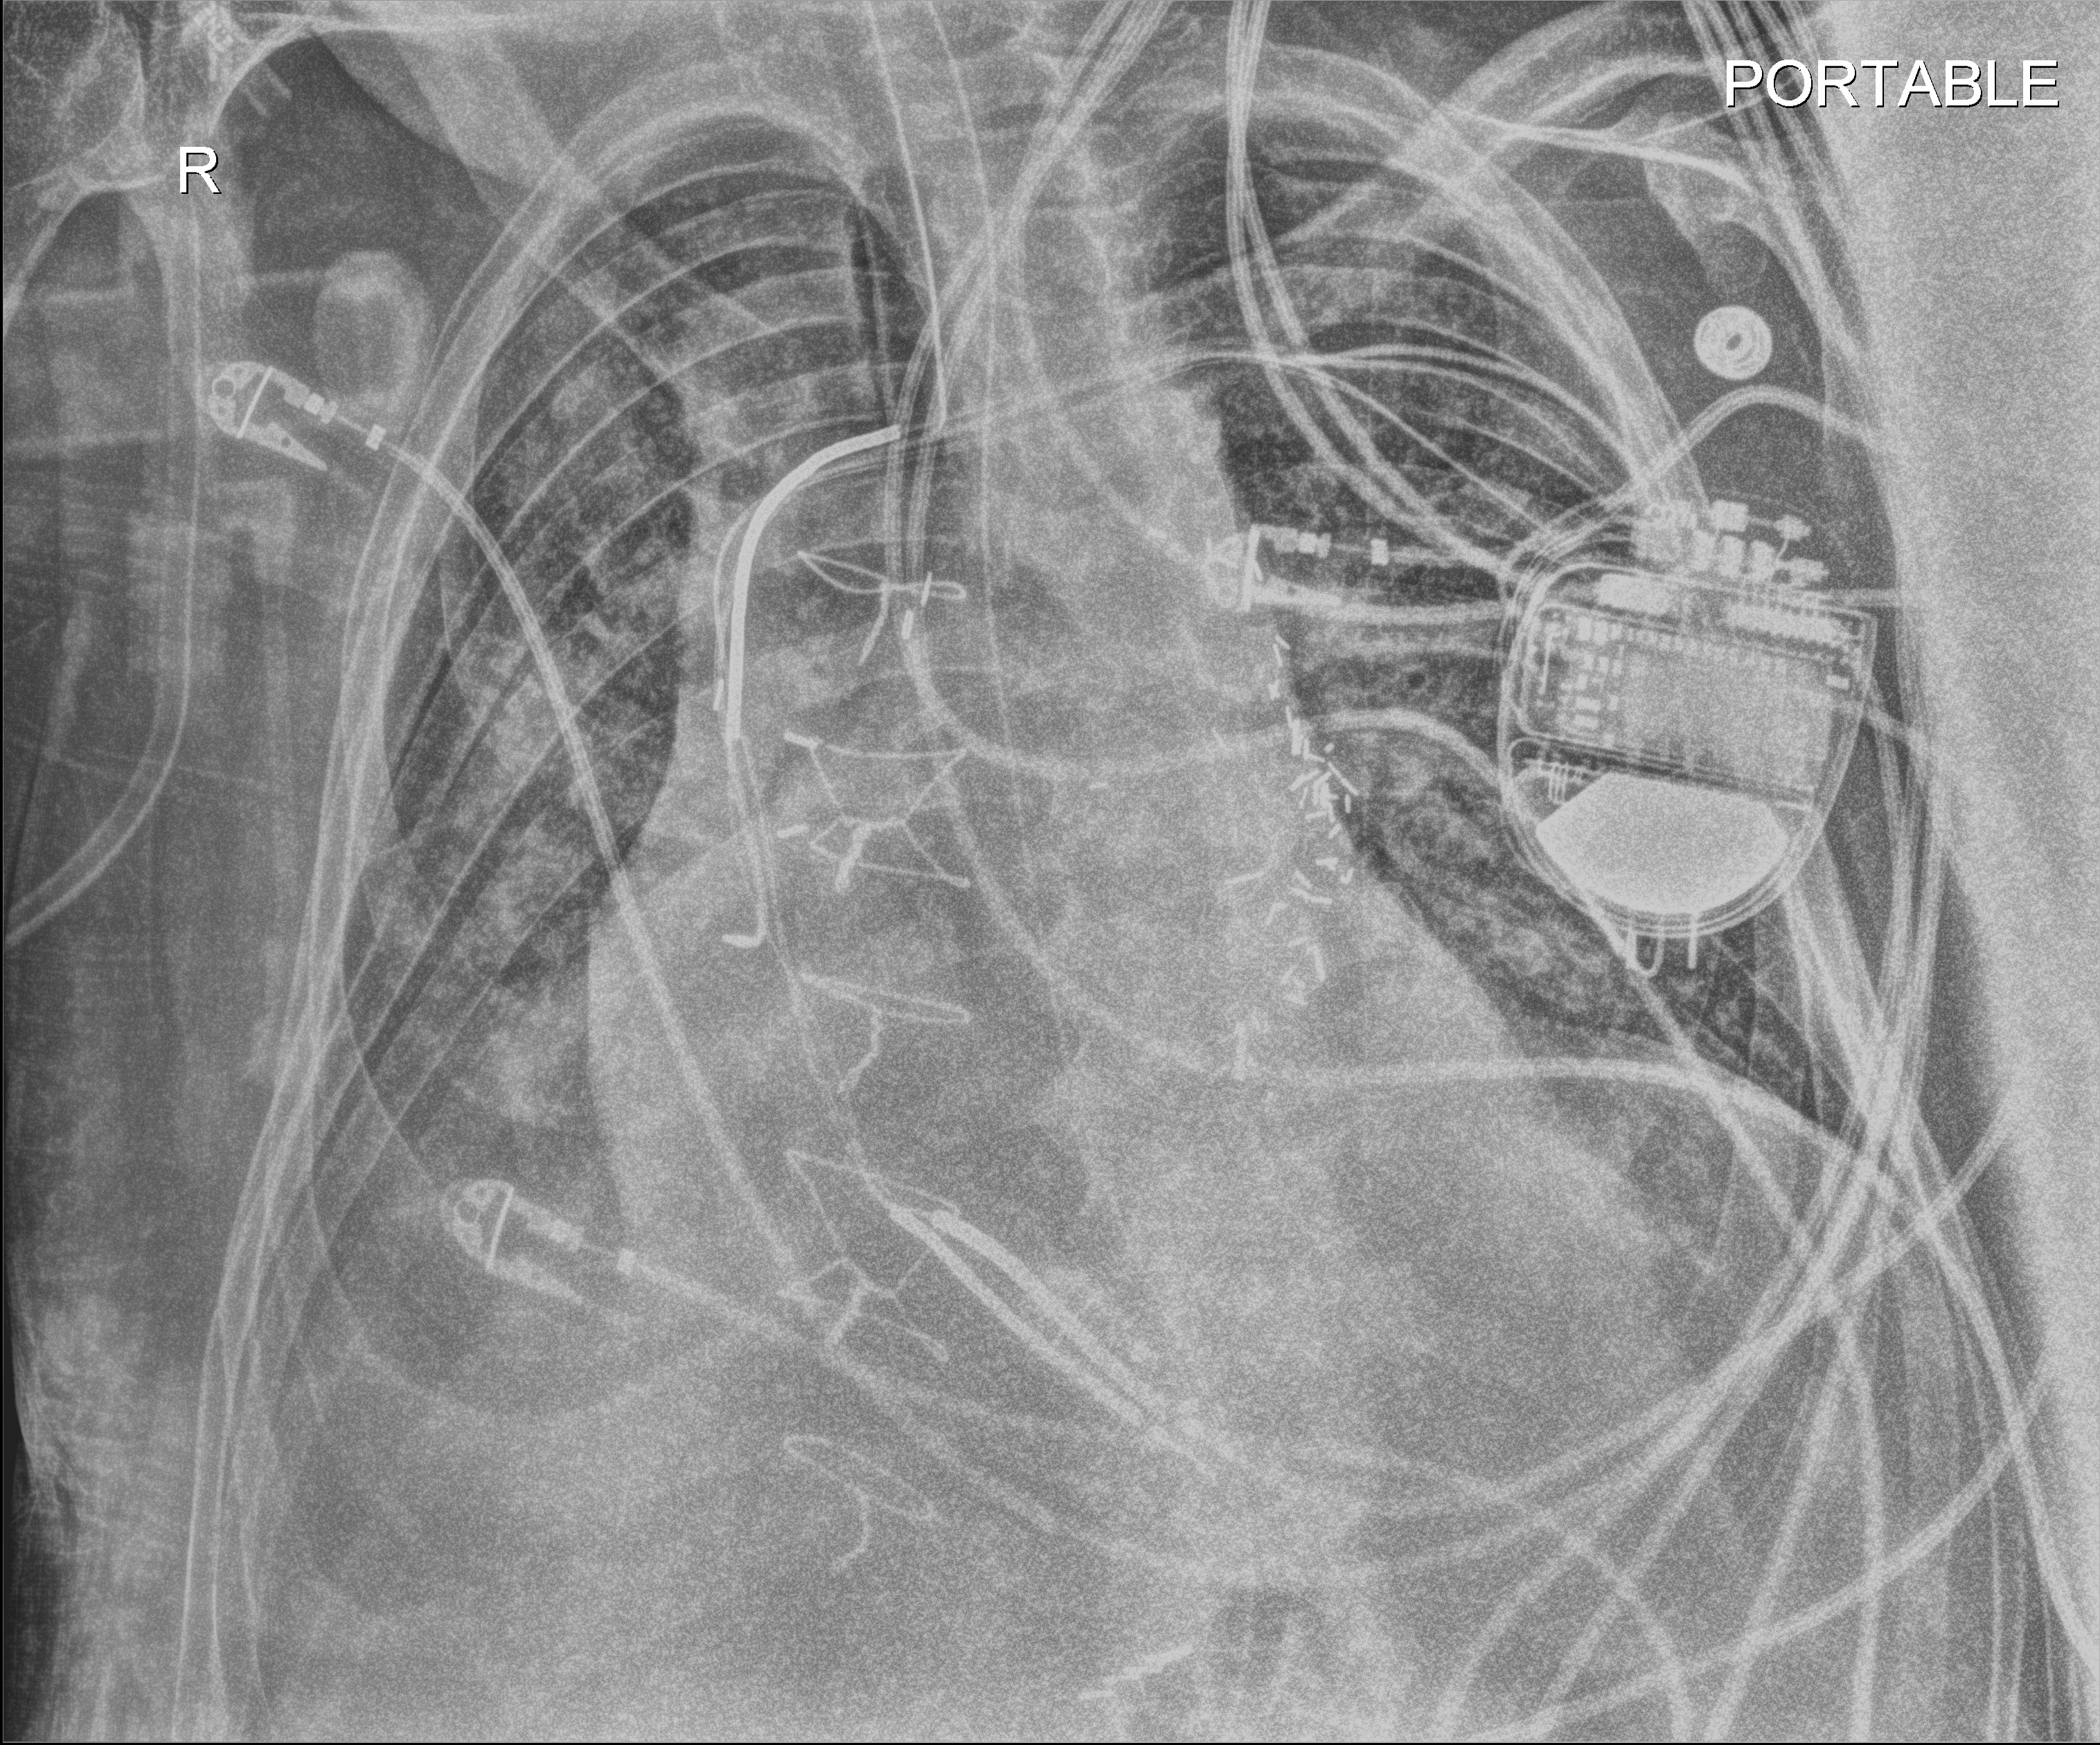
Portable chest radiograph; anteroposterior (AP) projection. Male patient hospitalised with COVID-19, age 60–74 years.
Hospital-stay facts (about this admission, not read from this image; timing relative to this image not recorded): admitted to intensive care during this hospital stay: yes.